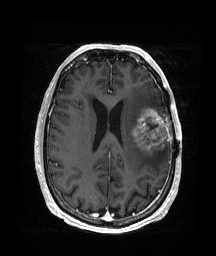
Brain MRI from a brain-tumour surgery series, one axial slice; position 73 of 176 along the scan axis; T1-weighted post-contrast; 216 × 256 image matrix, field of view 219 × 260 mm. From the clinical record (not read from this slice): histopathology: Glioblastoma; WHO grade: 4; IDH mutation: no.
Structures marked on this image (manually delineated by an expert):
- tumour: bounding box <132,108,168,155> (left, top, right, bottom; pixels)